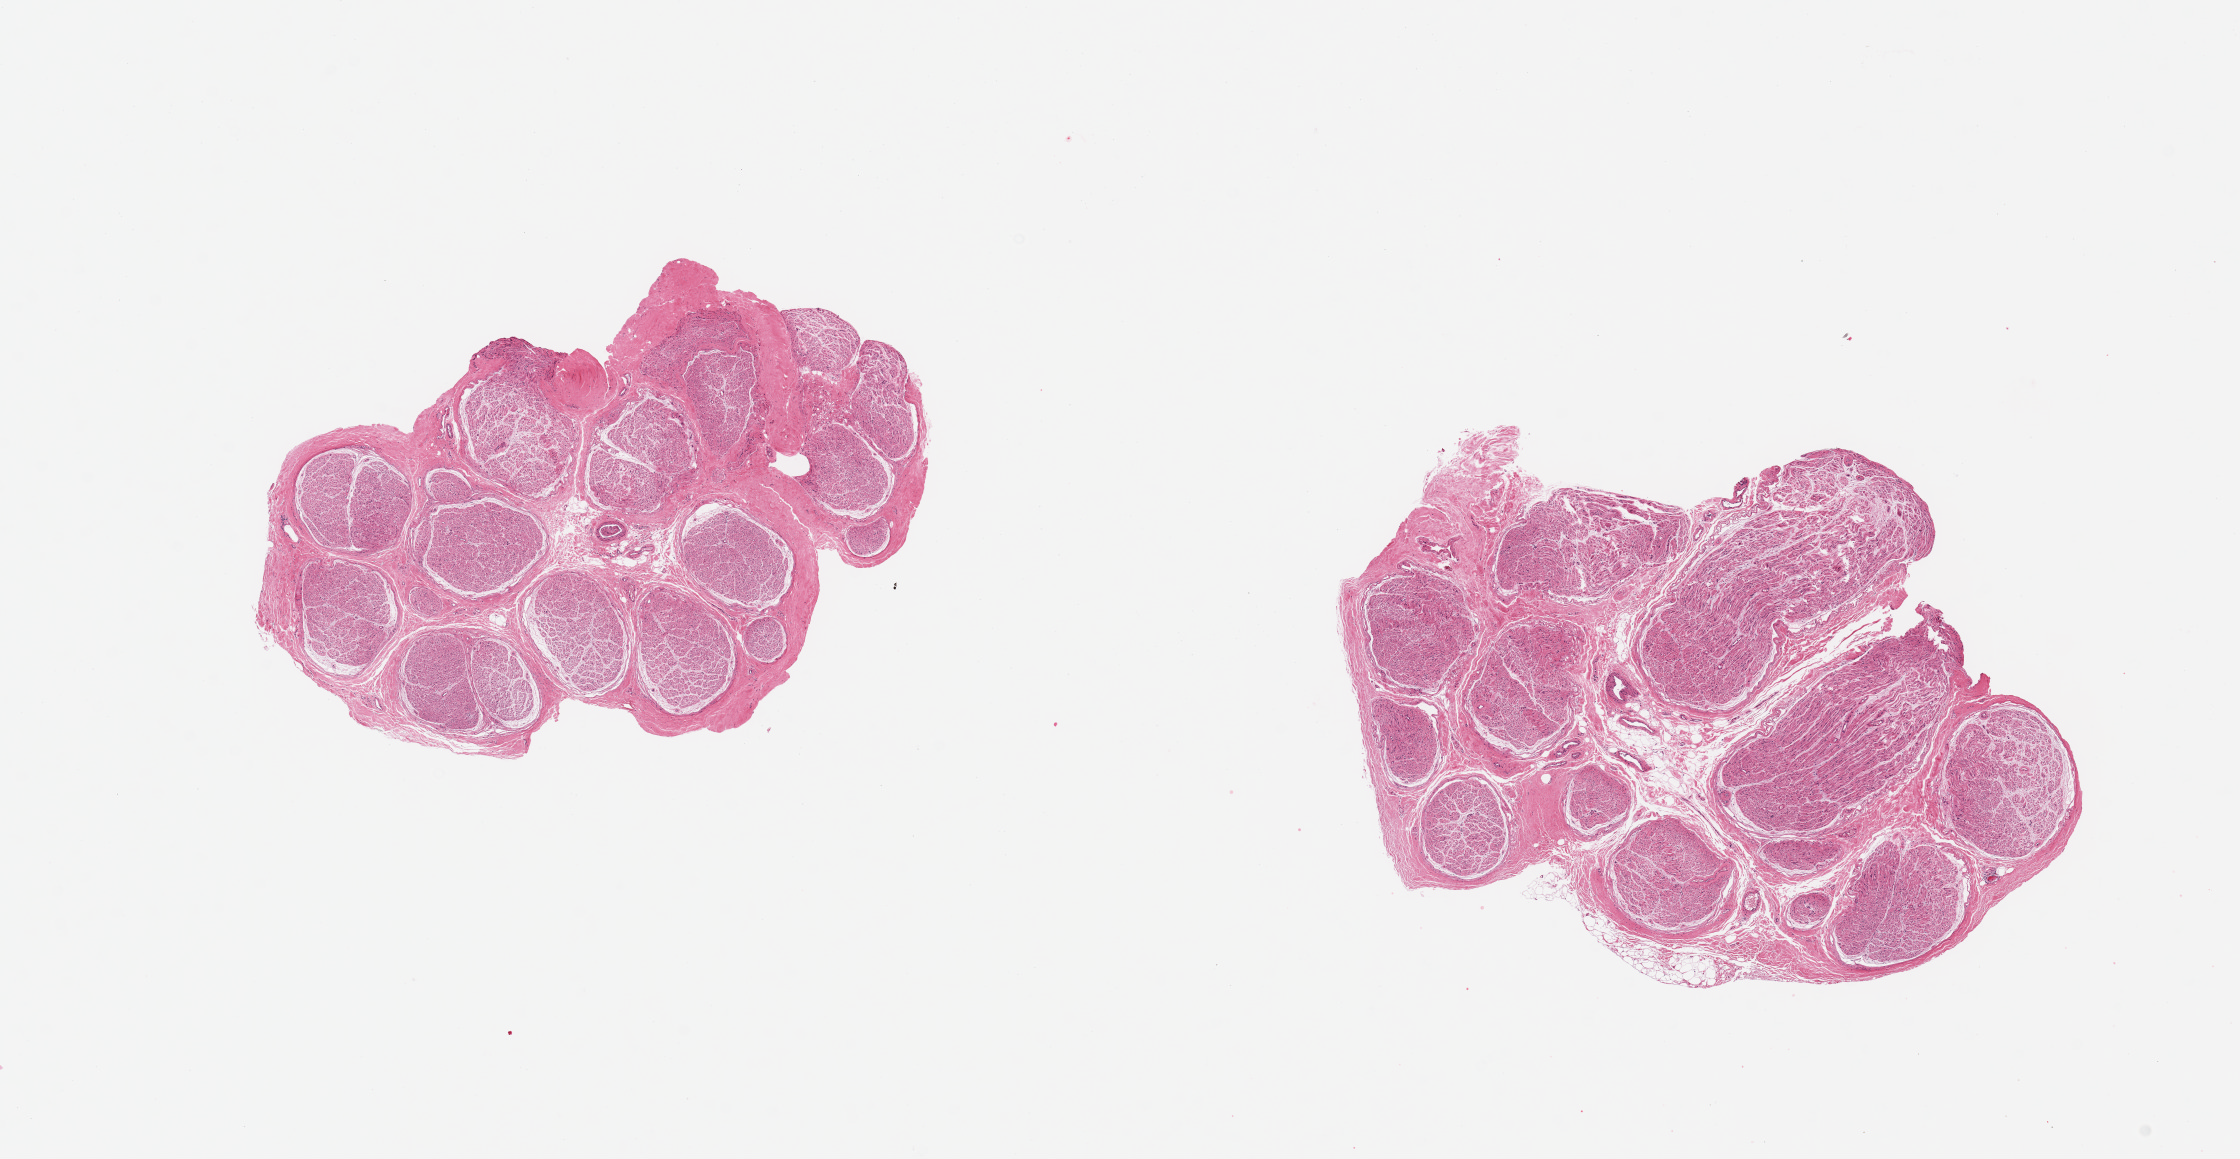
Digitized H&E-stained section — shown as a low-resolution overview of the whole scanned area (about 17.7 x 9.2 mm, acquisition: 20x scan), PAXgene-fixed paraffin-embedded (PFPE) section, section of tibial nerve (target tissue), donor tissue sample. Donor sex: male.
Reviewer comment on this tissue sample: 2 pieces, no adherent fat.